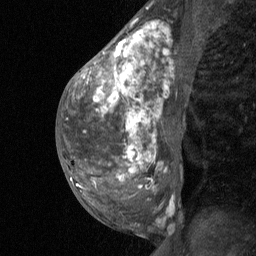
Breast MRI (dynamic contrast-enhanced), one sagittal slice. Slice 32 of 64 in the series (ordered by position). Dynamic contrast-enhanced study with each time point stored as its own series, time point 2 of 3 at this slice position (early post-contrast, ordered by acquisition time). 1.5 T. TE 4.8 ms, TR 27 ms. 2 mm slice thickness. 256 × 256 image matrix, field of view 180 × 180 mm. Patient: female, 36 years. Case-level facts recorded for this patient, not image findings: setting: breast cancer imaged before/during neoadjuvant chemotherapy; receptor status: HR-positive, HER2-negative.
Annotated regions visible in this slice (semi-automatically segmented with operator editing):
- analysis volume of interest (the breast-tissue region the enhancement analysis was run in; not a lesion): bounding box <67,12,187,238> (left, top, right, bottom; pixels)
- tumour enhancement mask (voxels above the 90 % enhancement threshold inside the analysis volume of interest): <94,26,152,181>